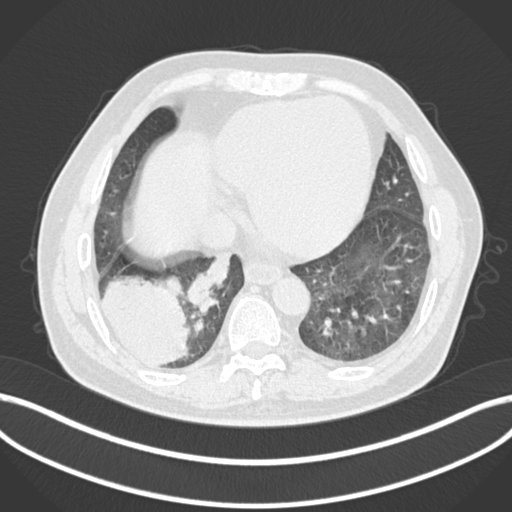
Chest CT, one axial slice. Position 41 of 200 along the scan axis. Lung window (W 1500 / L -600 HU). 1 mm slice thickness. 512 × 512 image matrix, field of view 400 × 400 mm. Male patient, age 59 years.
Outlined on this slice (bounding box drawn by a radiologist):
- lung tumour (recorded histology: adenocarcinoma): bounding box [x1, y1, x2, y2] px = [95, 271, 191, 368]